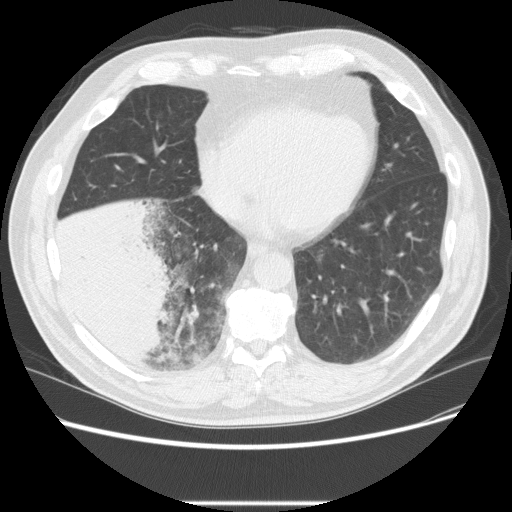
Low-dose screening chest CT, one axial slice; position 77 of 233 along the scan axis; reconstruction kernel STANDARD; lung window (W 1500 / L -600 HU); 2.5 mm slice thickness; 512 × 512 image matrix.
Structures marked on this image (outlined manually by an expert reader):
- lesion 3 (tumor, lower lobe of right lung): bounding box [x1, y1, x2, y2] px = [54, 199, 177, 366]